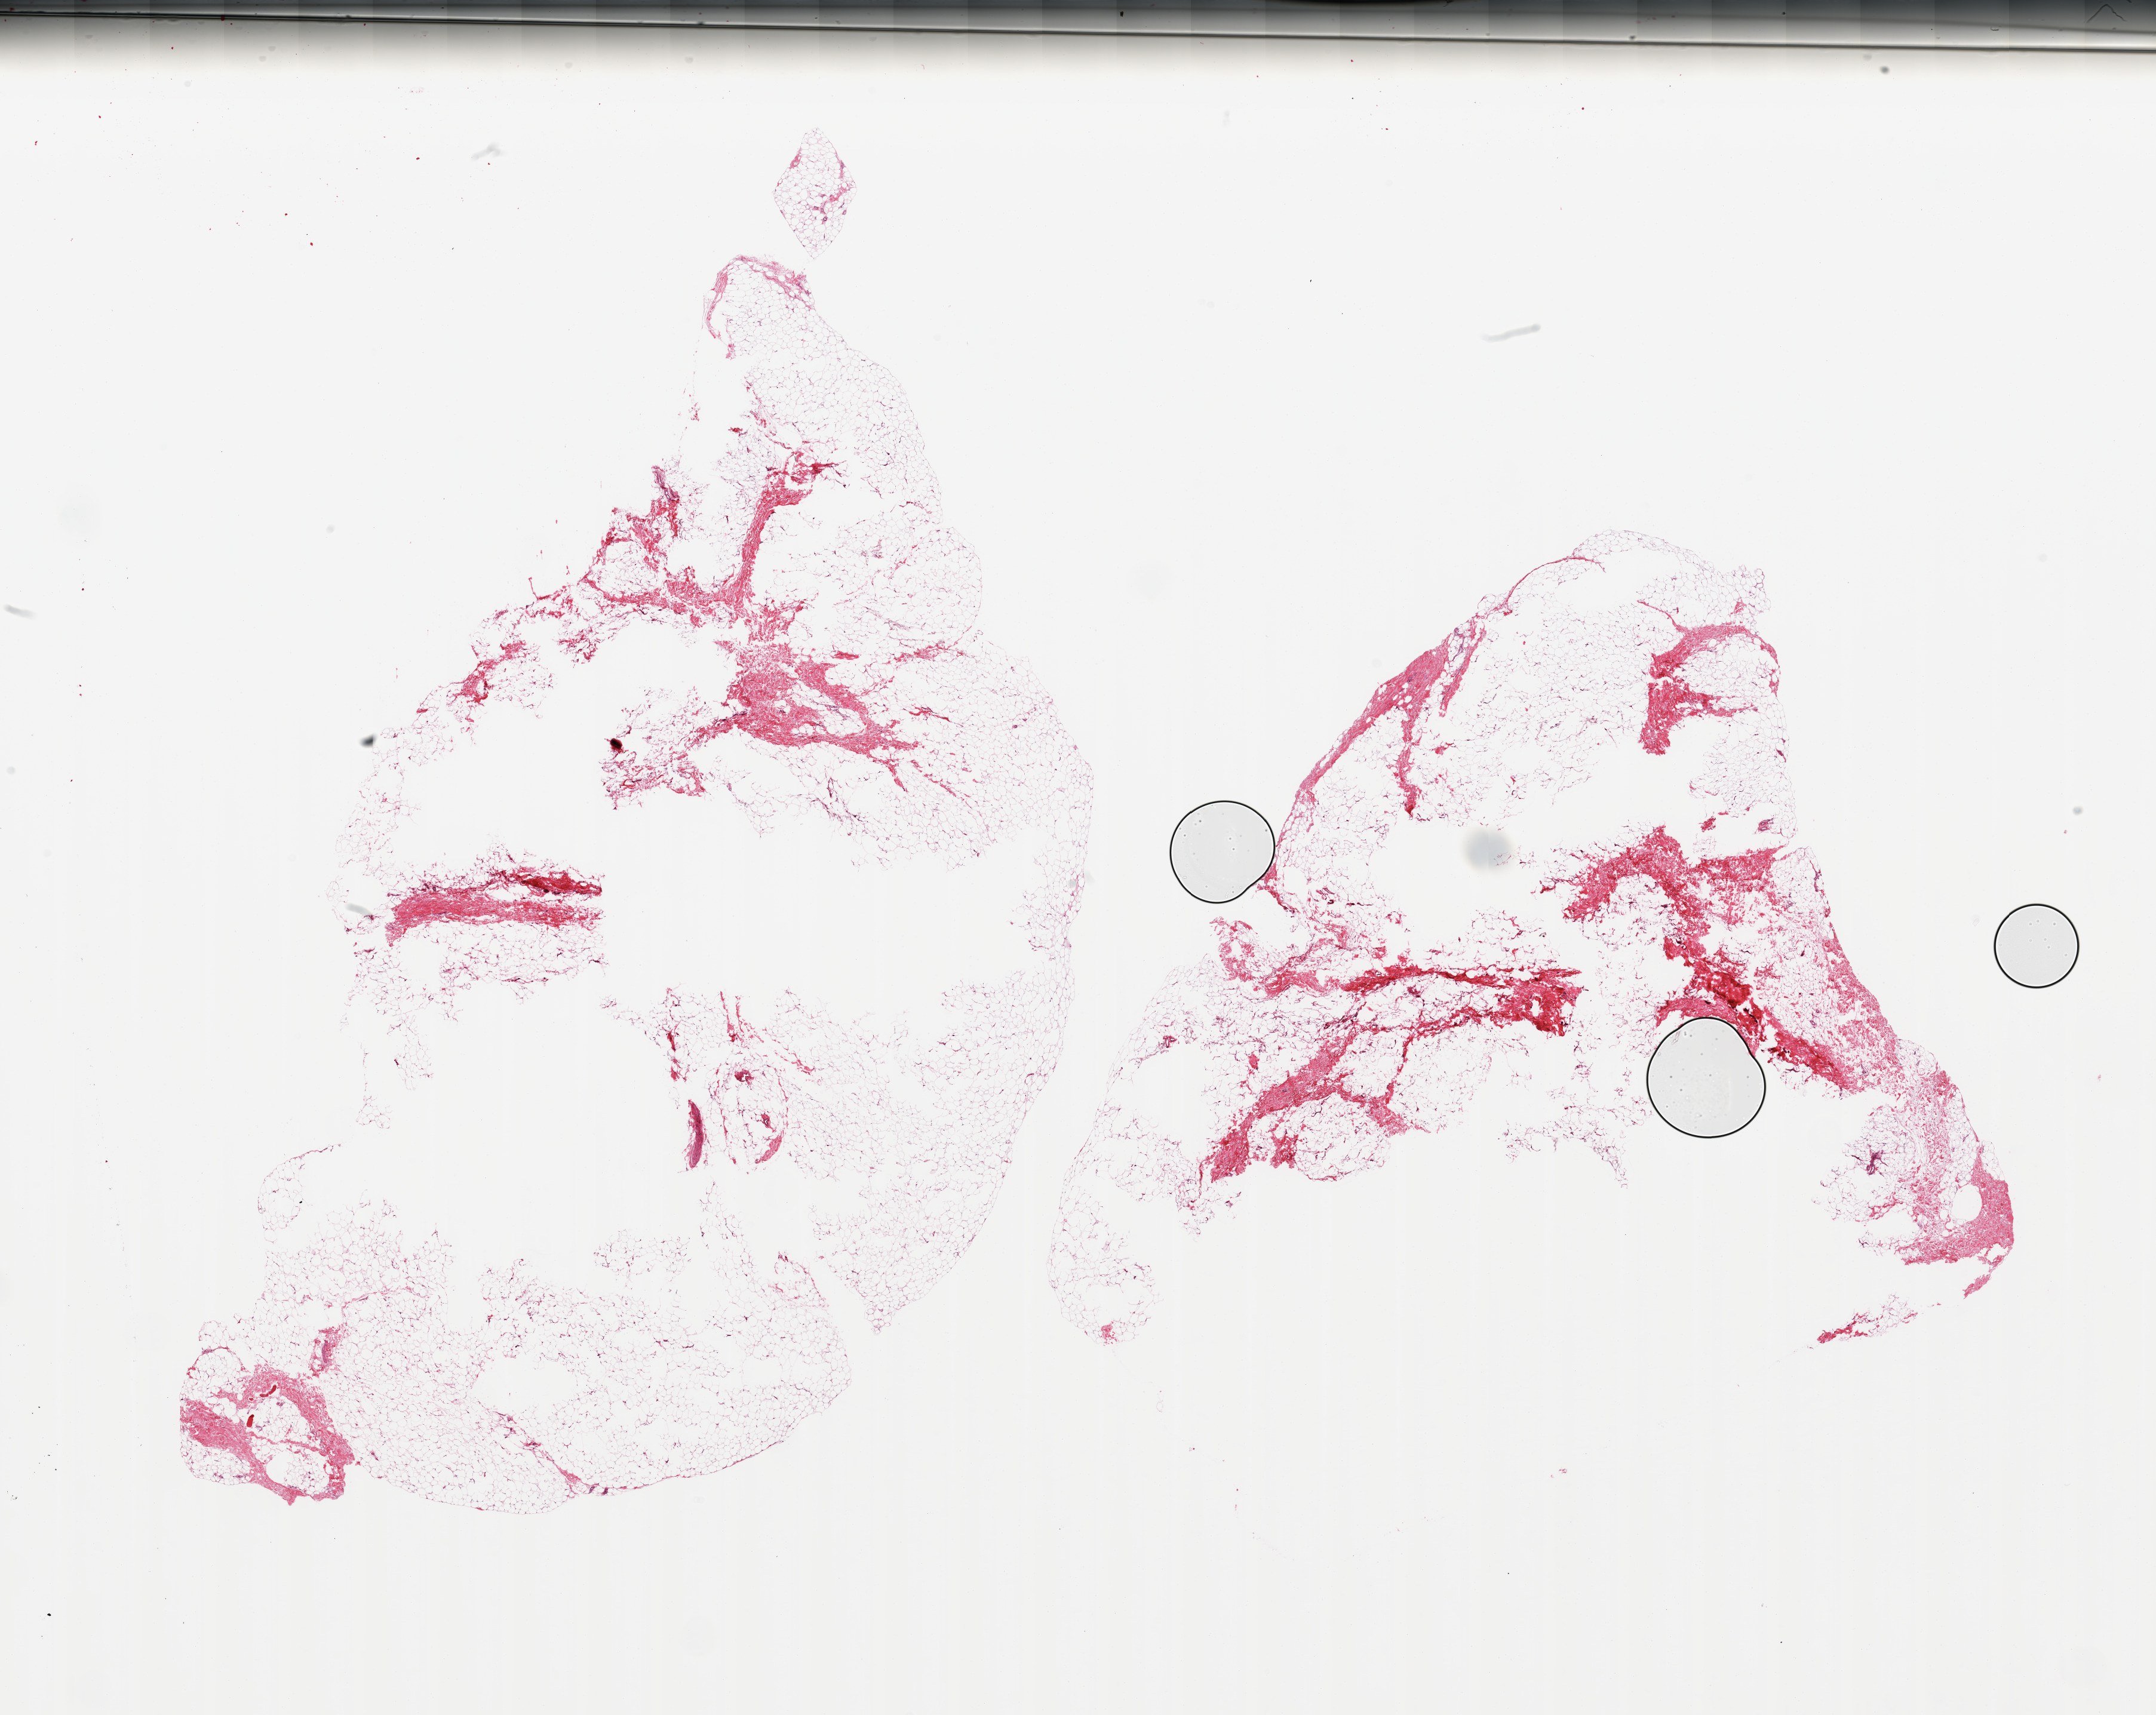
Whole-slide image, hematoxylin and eosin (H&E) stain, low-resolution overview of the scanned area, about 28.5 x 22.7 mm (slide scanned at 20x); PAXgene-fixed paraffin-embedded (PFPE) section; section of breast (target tissue); donor tissue sample. Donor: male.
Review note (as recorded): 2 pieces; fibrofatty tissue without mammary ducts.